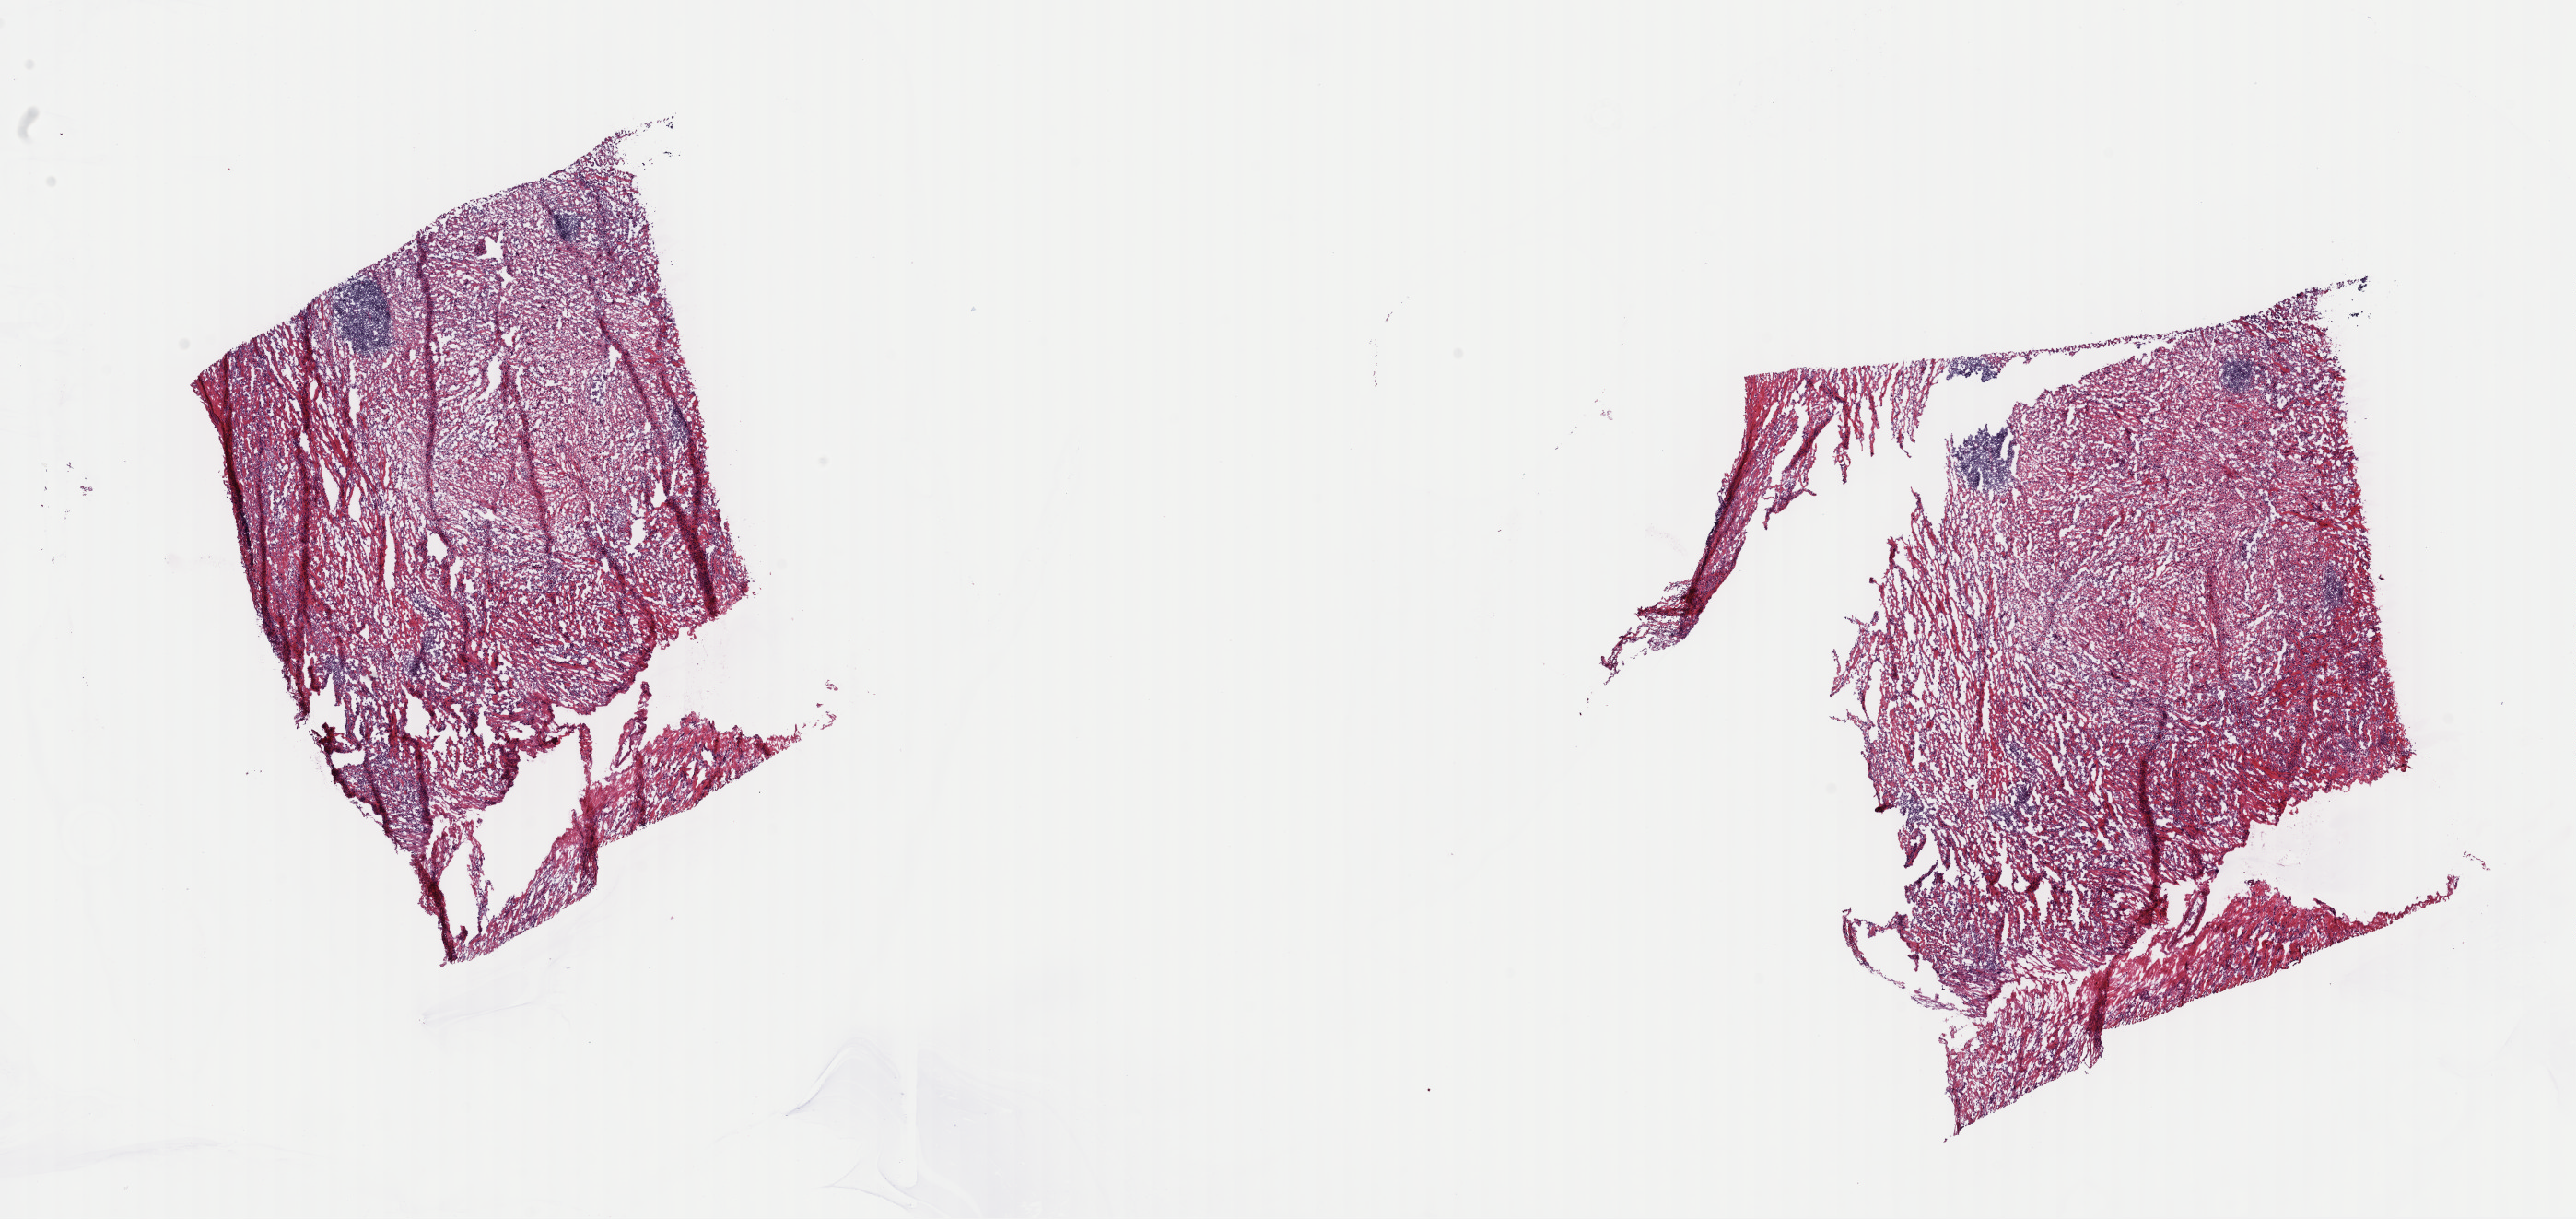
Whole-slide histology image, H&E — a low-resolution overview of the entire scanned area, about 22.1 x 10.5 mm (acquisition: 40x scan). Frozen section from the top of the tissue portion. Primary tumour sample from the mesothelium. Male, age 55 years at initial diagnosis. Composition of this section per pathologist review: tumour cells 30%, tumour nuclei 85%, normal cells 0%, stromal cells 70%, necrosis 0%. Infiltration values recorded for this section: lymphocyte infiltration 15%, monocyte infiltration 0%, neutrophil infiltration 0%.
AJCC pathologic stage: I. Histologic diagnosis: Epithelioid mesothelioma, malignant (pleura, NOS). TNM: T1 N0 M0.